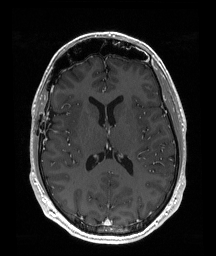
Brain MRI from a brain-tumour surgery series, one axial slice. Slice 94 of 192 in the series (ordered by position). T1-weighted post-contrast. 1 mm slice thickness. 216 × 256 image matrix, field of view 219 × 260 mm. Case-level facts recorded for this patient, not image findings: histopathology: Astrocytoma; WHO grade: 2; IDH mutation: yes; tumour location: Right Insular.
Annotated regions visible in this slice (manually delineated by an expert):
- tumour: bounding box [x1, y1, x2, y2] px = [73, 113, 78, 119]